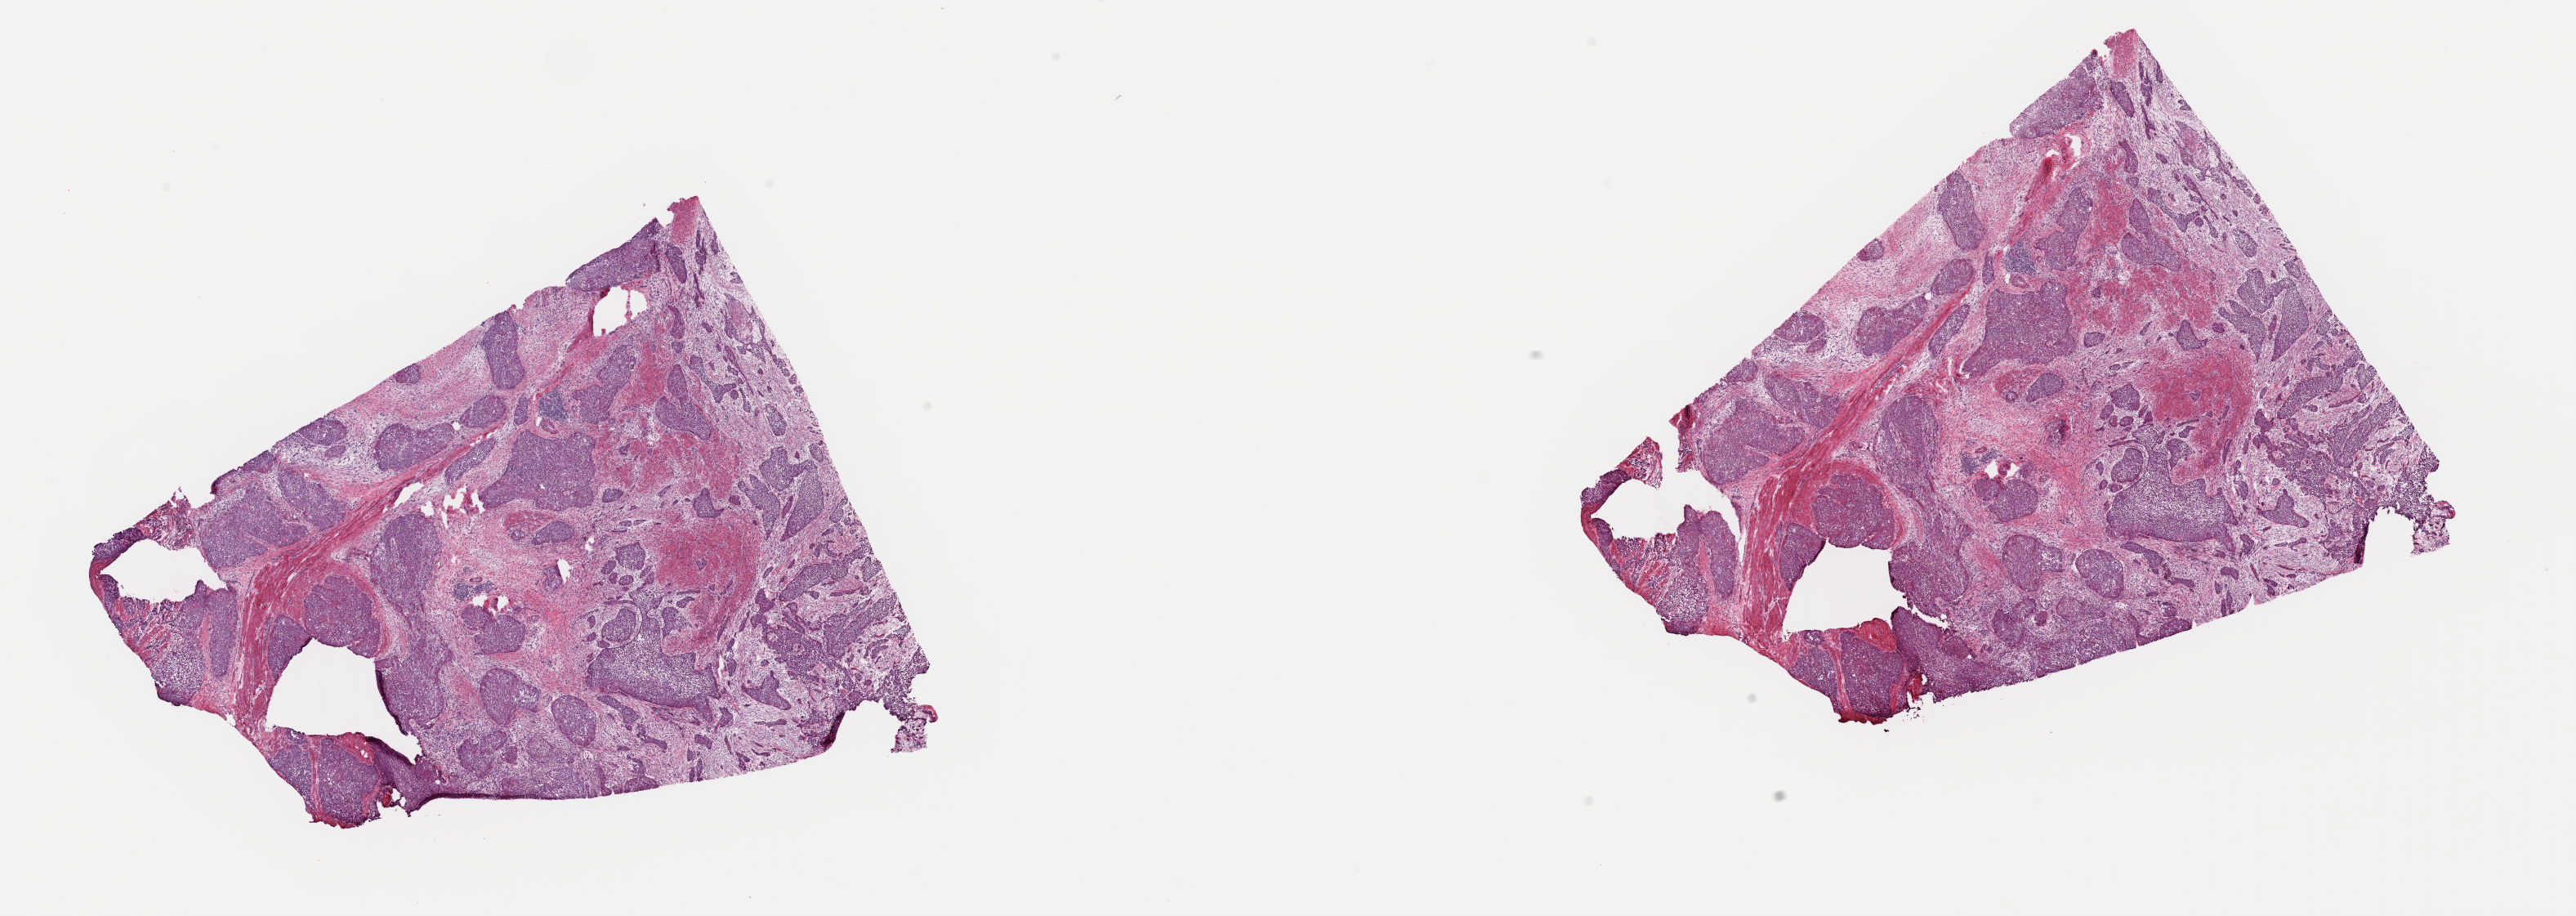
Digitized H&E-stained tissue section (whole slide), whole scanned area (about 24.9 x 8.9 mm, from a 40x scan) shown as a low-resolution overview, frozen section, primary tumour sample from the bladder. Male patient; age at initial diagnosis 76 years. Histologic grade: high grade. Composition of this section per pathologist review: tumour cells 45%, tumour nuclei 85%, normal cells 0%, stromal cells 54%, necrosis 1%. Inflammatory infiltration, as recorded: lymphocyte infiltration 5%, monocyte infiltration 1%, neutrophil infiltration 1%.
Diagnosis: Transitional cell carcinoma. AJCC pathologic stage: IV (7th edition).